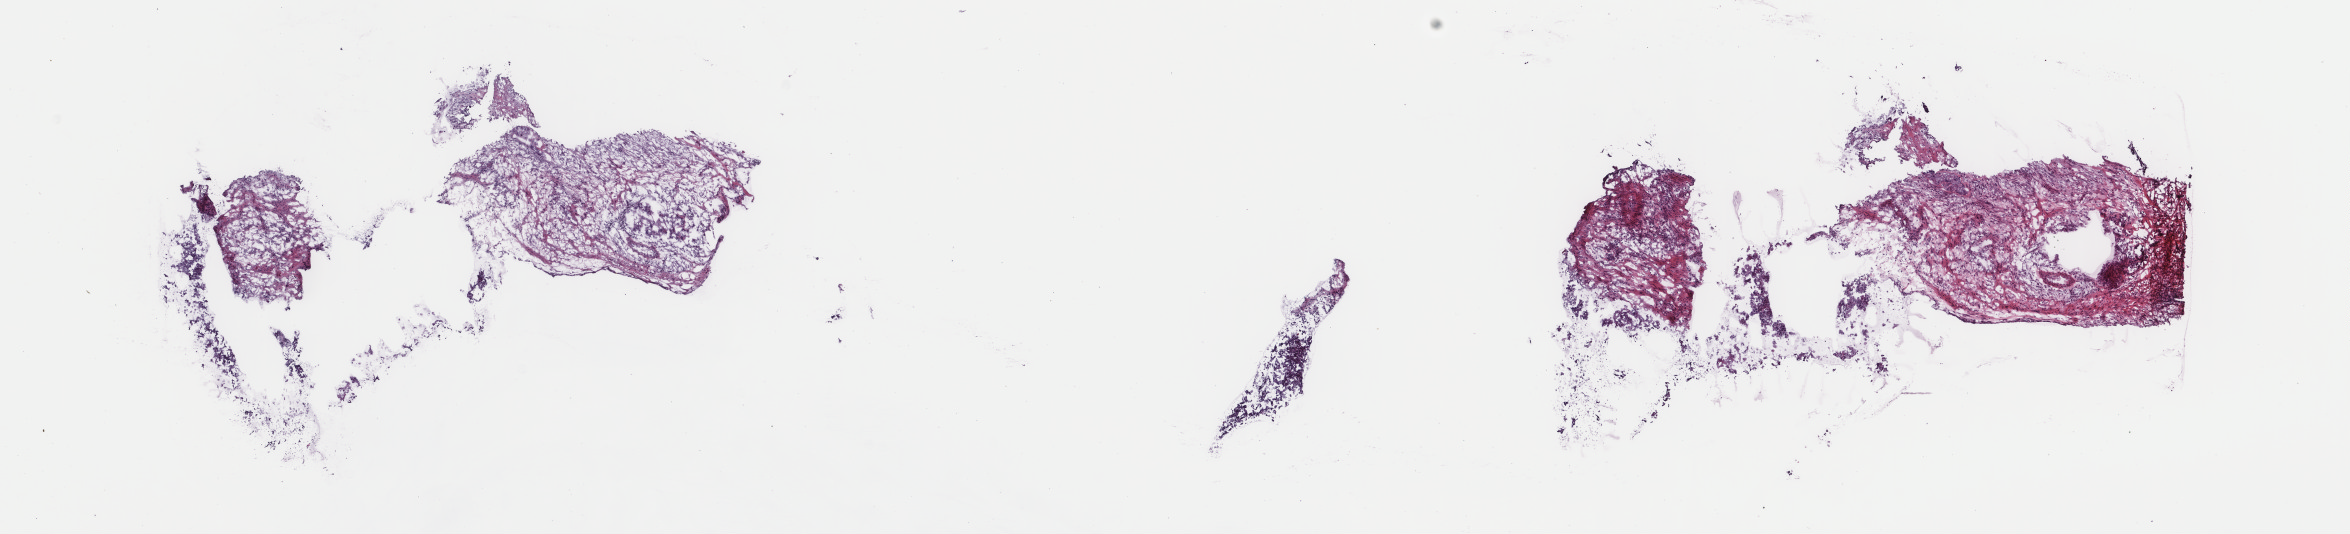
Digitized Hematoxylin and eosin (H&E) stained tissue section (whole slide), low-resolution overview of the scanned area, about 18.7 x 4.2 mm (acquisition: 40x scan). Frozen section. Sample: primary tumour, uterus. Female patient; age at initial diagnosis 51 years. Composition of this section per pathologist review: tumour cells 100%, tumour nuclei 60%, normal cells 0%, stromal cells 0%, necrosis 0%. Inflammatory infiltration, as recorded: lymphocyte infiltration 1%, monocyte infiltration 0%, neutrophil infiltration 0%.
FIGO stage: IB. Pathologic diagnosis: Mullerian mixed tumor.